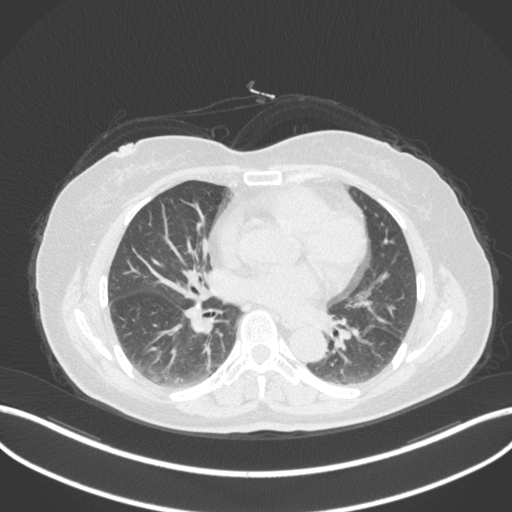
Chest CT, one axial slice; position 177 of 307 along the scan axis; reconstruction kernel B31f; lung window (W 1500 / L -600 HU); 1 mm slice thickness; 512 × 512 image matrix, field of view 400 × 400 mm. Female patient, age 59 years. Case-level facts recorded for this patient, not image findings: clinical TNM (as recorded): T2a N0 M0.
Annotated regions visible in this slice (bounding box drawn by a radiologist):
- lung tumour (recorded histology: adenocarcinoma): box from (x=354, y=328) to (x=378, y=357) px